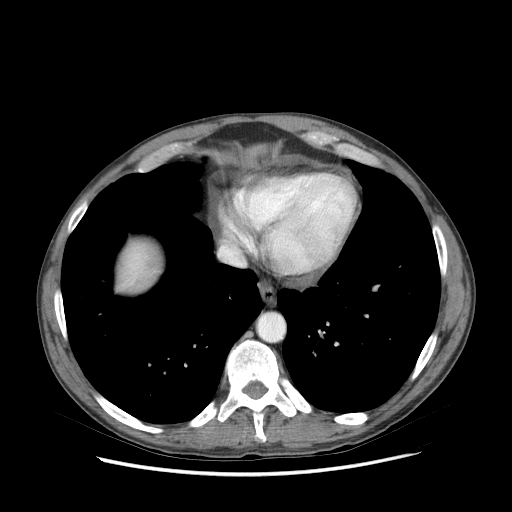
Contrast-enhanced abdominal CT (liver protocol), one axial slice; position 76 of 89 along the scan axis; reconstruction kernel STANDARD; 140 kVp; soft-tissue window (W 400 / L 40 HU); 512 × 512 image matrix. From the clinical record (not read from this slice): diagnosis: hepatocellular carcinoma (patient treated with transarterial chemoembolisation; whether this scan precedes or follows treatment is not stated here); TNM stage (as recorded): Stage-IIIB; Child-Pugh class: A; tumour differentiation: moderately differentiated.
Annotated regions visible in this slice (semi-automatic segmentation, software-assisted and operator-edited):
- liver parenchyma outside the tumour (the mass and vessels are separate outlines, so this box may not span the whole liver): bounding box [x1, y1, x2, y2] px = [120, 246, 156, 290]